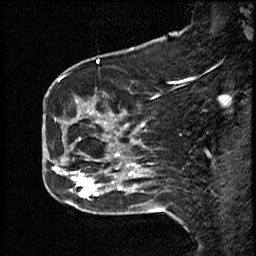
Breast MRI (dynamic contrast-enhanced), one sagittal slice. Position 17 of 50 along the scan axis. Dynamic contrast-enhanced study with each time point stored as its own series, time point 2 of 4 at this slice position (early post-contrast, ordered by acquisition time). 1.5 T. TE 4.2 ms, TR 18.5 ms. 3 mm slice thickness. 256 × 256 image matrix. Female patient, age 44 years. From the clinical record (not read from this slice): setting: breast cancer imaged before/during neoadjuvant chemotherapy; receptor status: HR-positive, HER2-negative.
Structures marked on this image (semi-automatically segmented with operator editing):
- analysis volume of interest (the breast-tissue region the enhancement analysis was run in; not a lesion): bounding box [x1, y1, x2, y2] px = [59, 80, 114, 206]
- tumour enhancement mask (voxels above the 100 % enhancement threshold inside the analysis volume of interest): [59, 80, 101, 198]